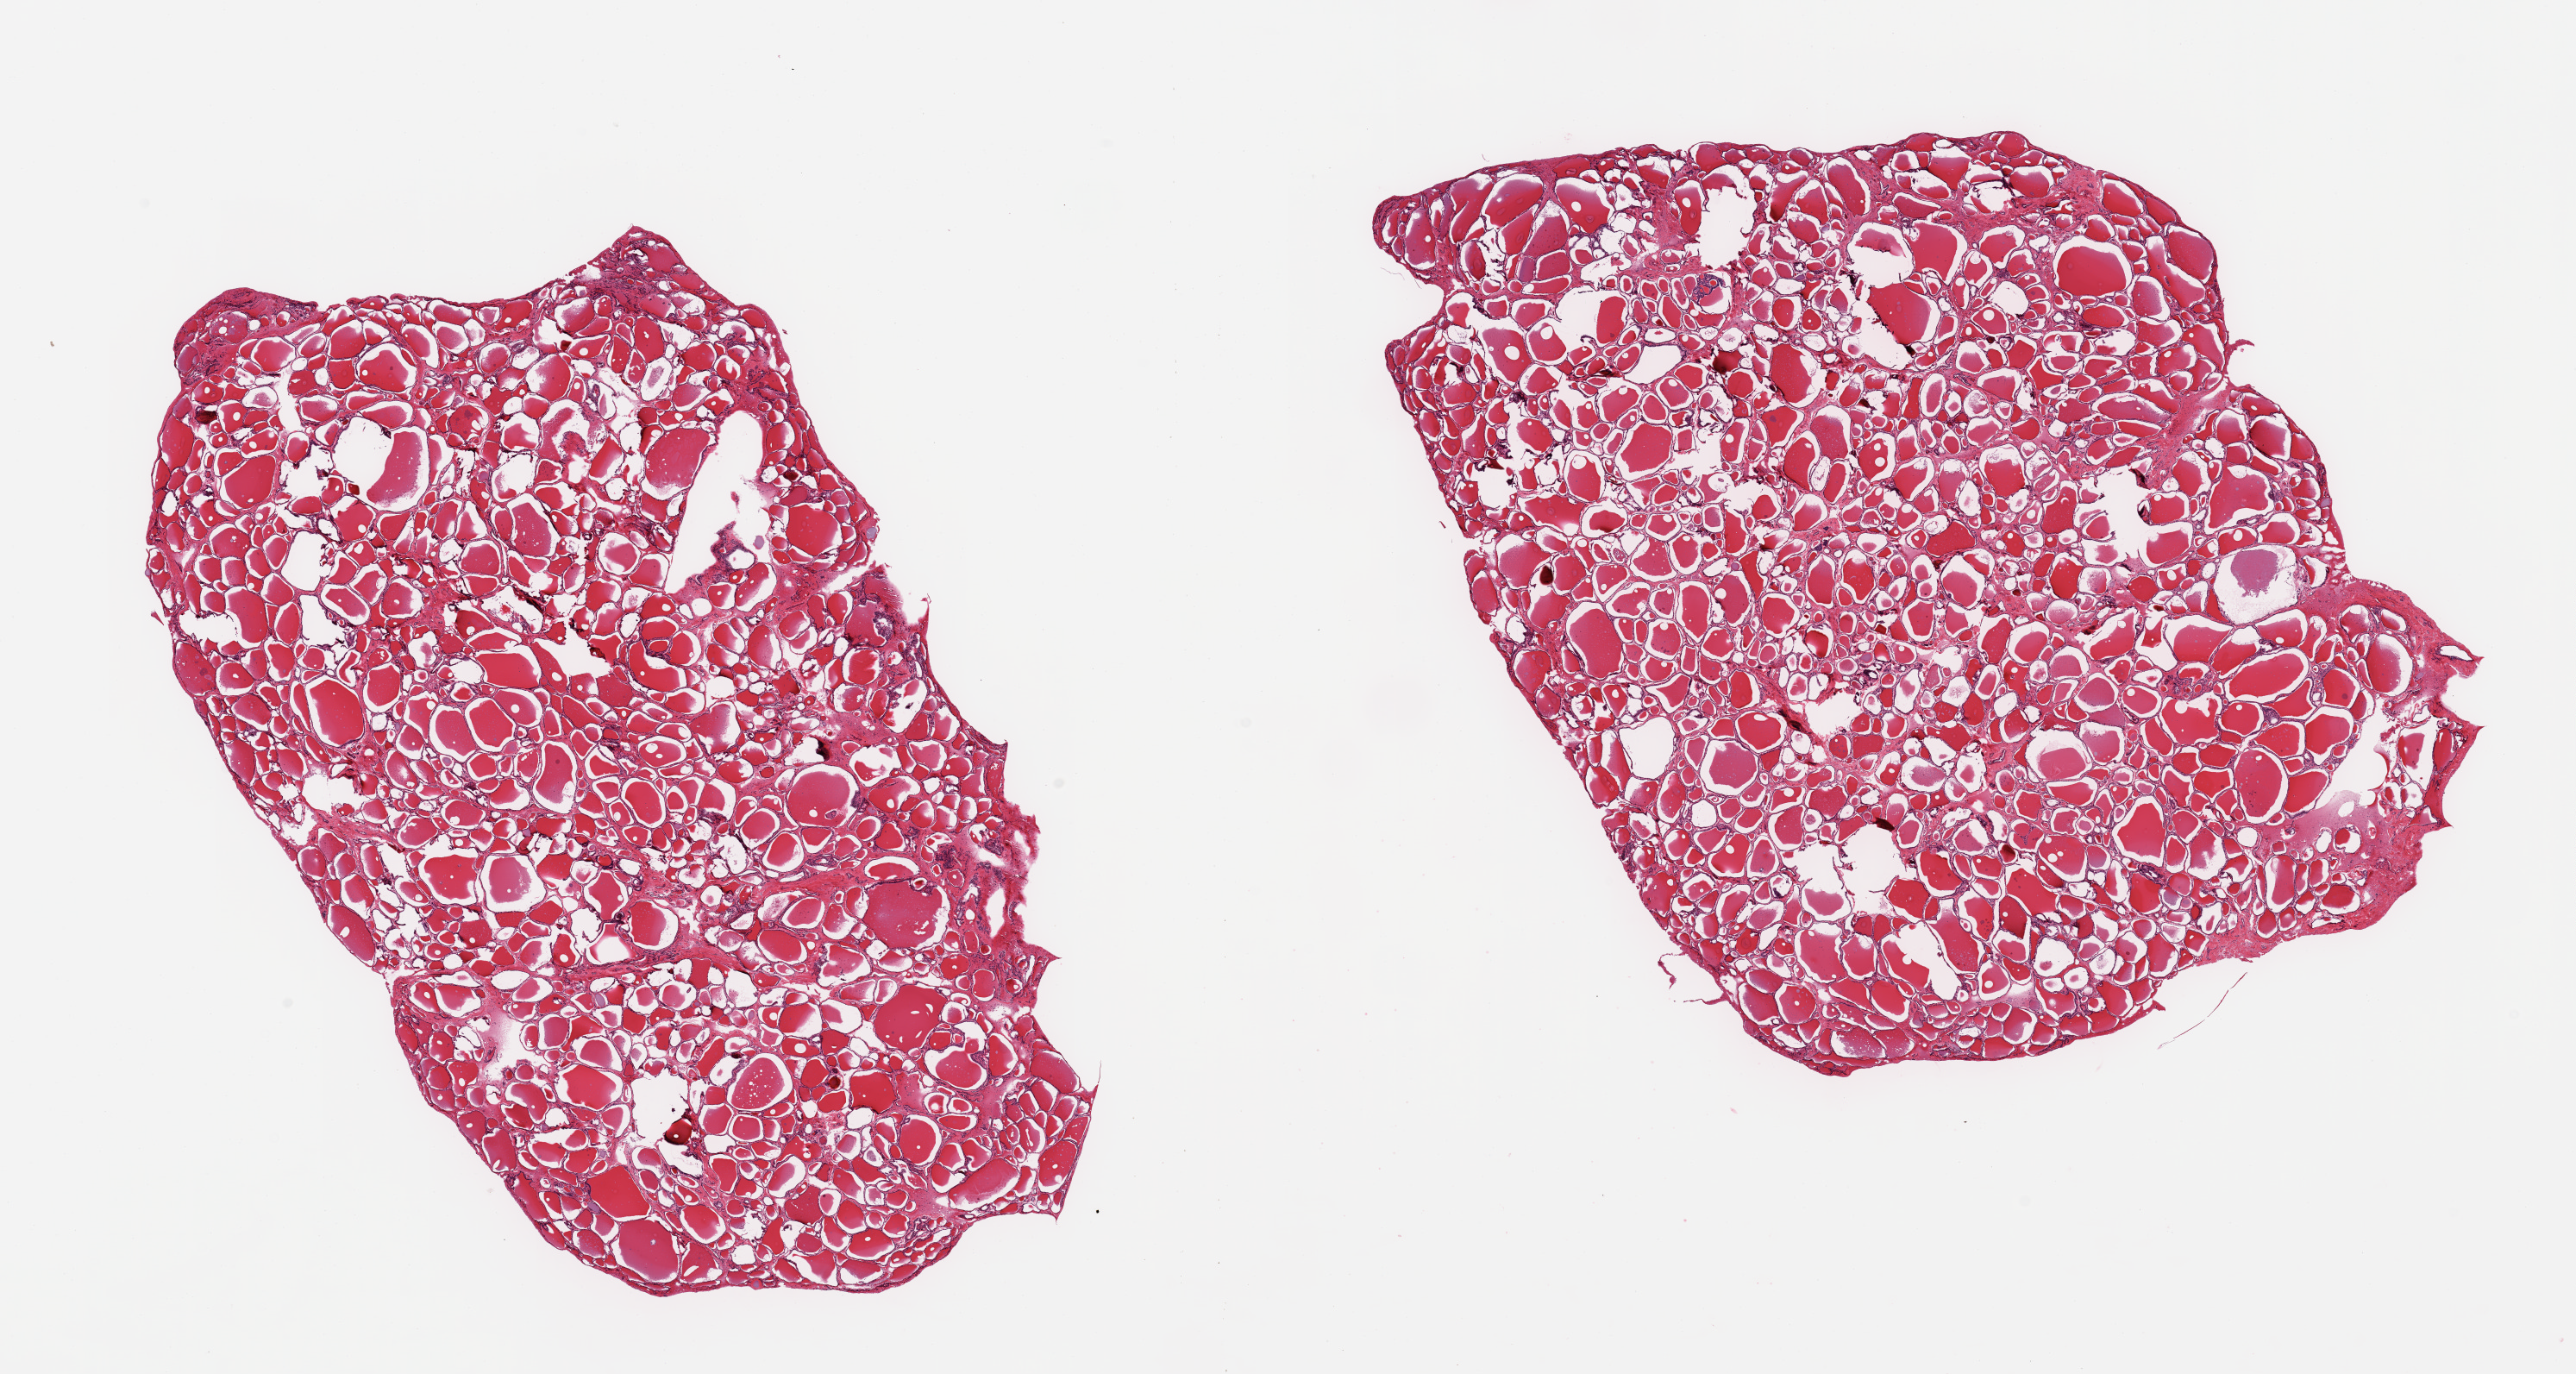
Digitized H&E-stained section, brightfield, low-resolution overview of the scanned area, about 23.6 x 12.6 mm (slide scanned at 20x), PAXgene-fixed, paraffin-embedded tissue, sampled site (target tissue): thyroid, tissue donor sample.
* reviewer comment on this tissue sample: 2 pieces; well preserved; no lesions